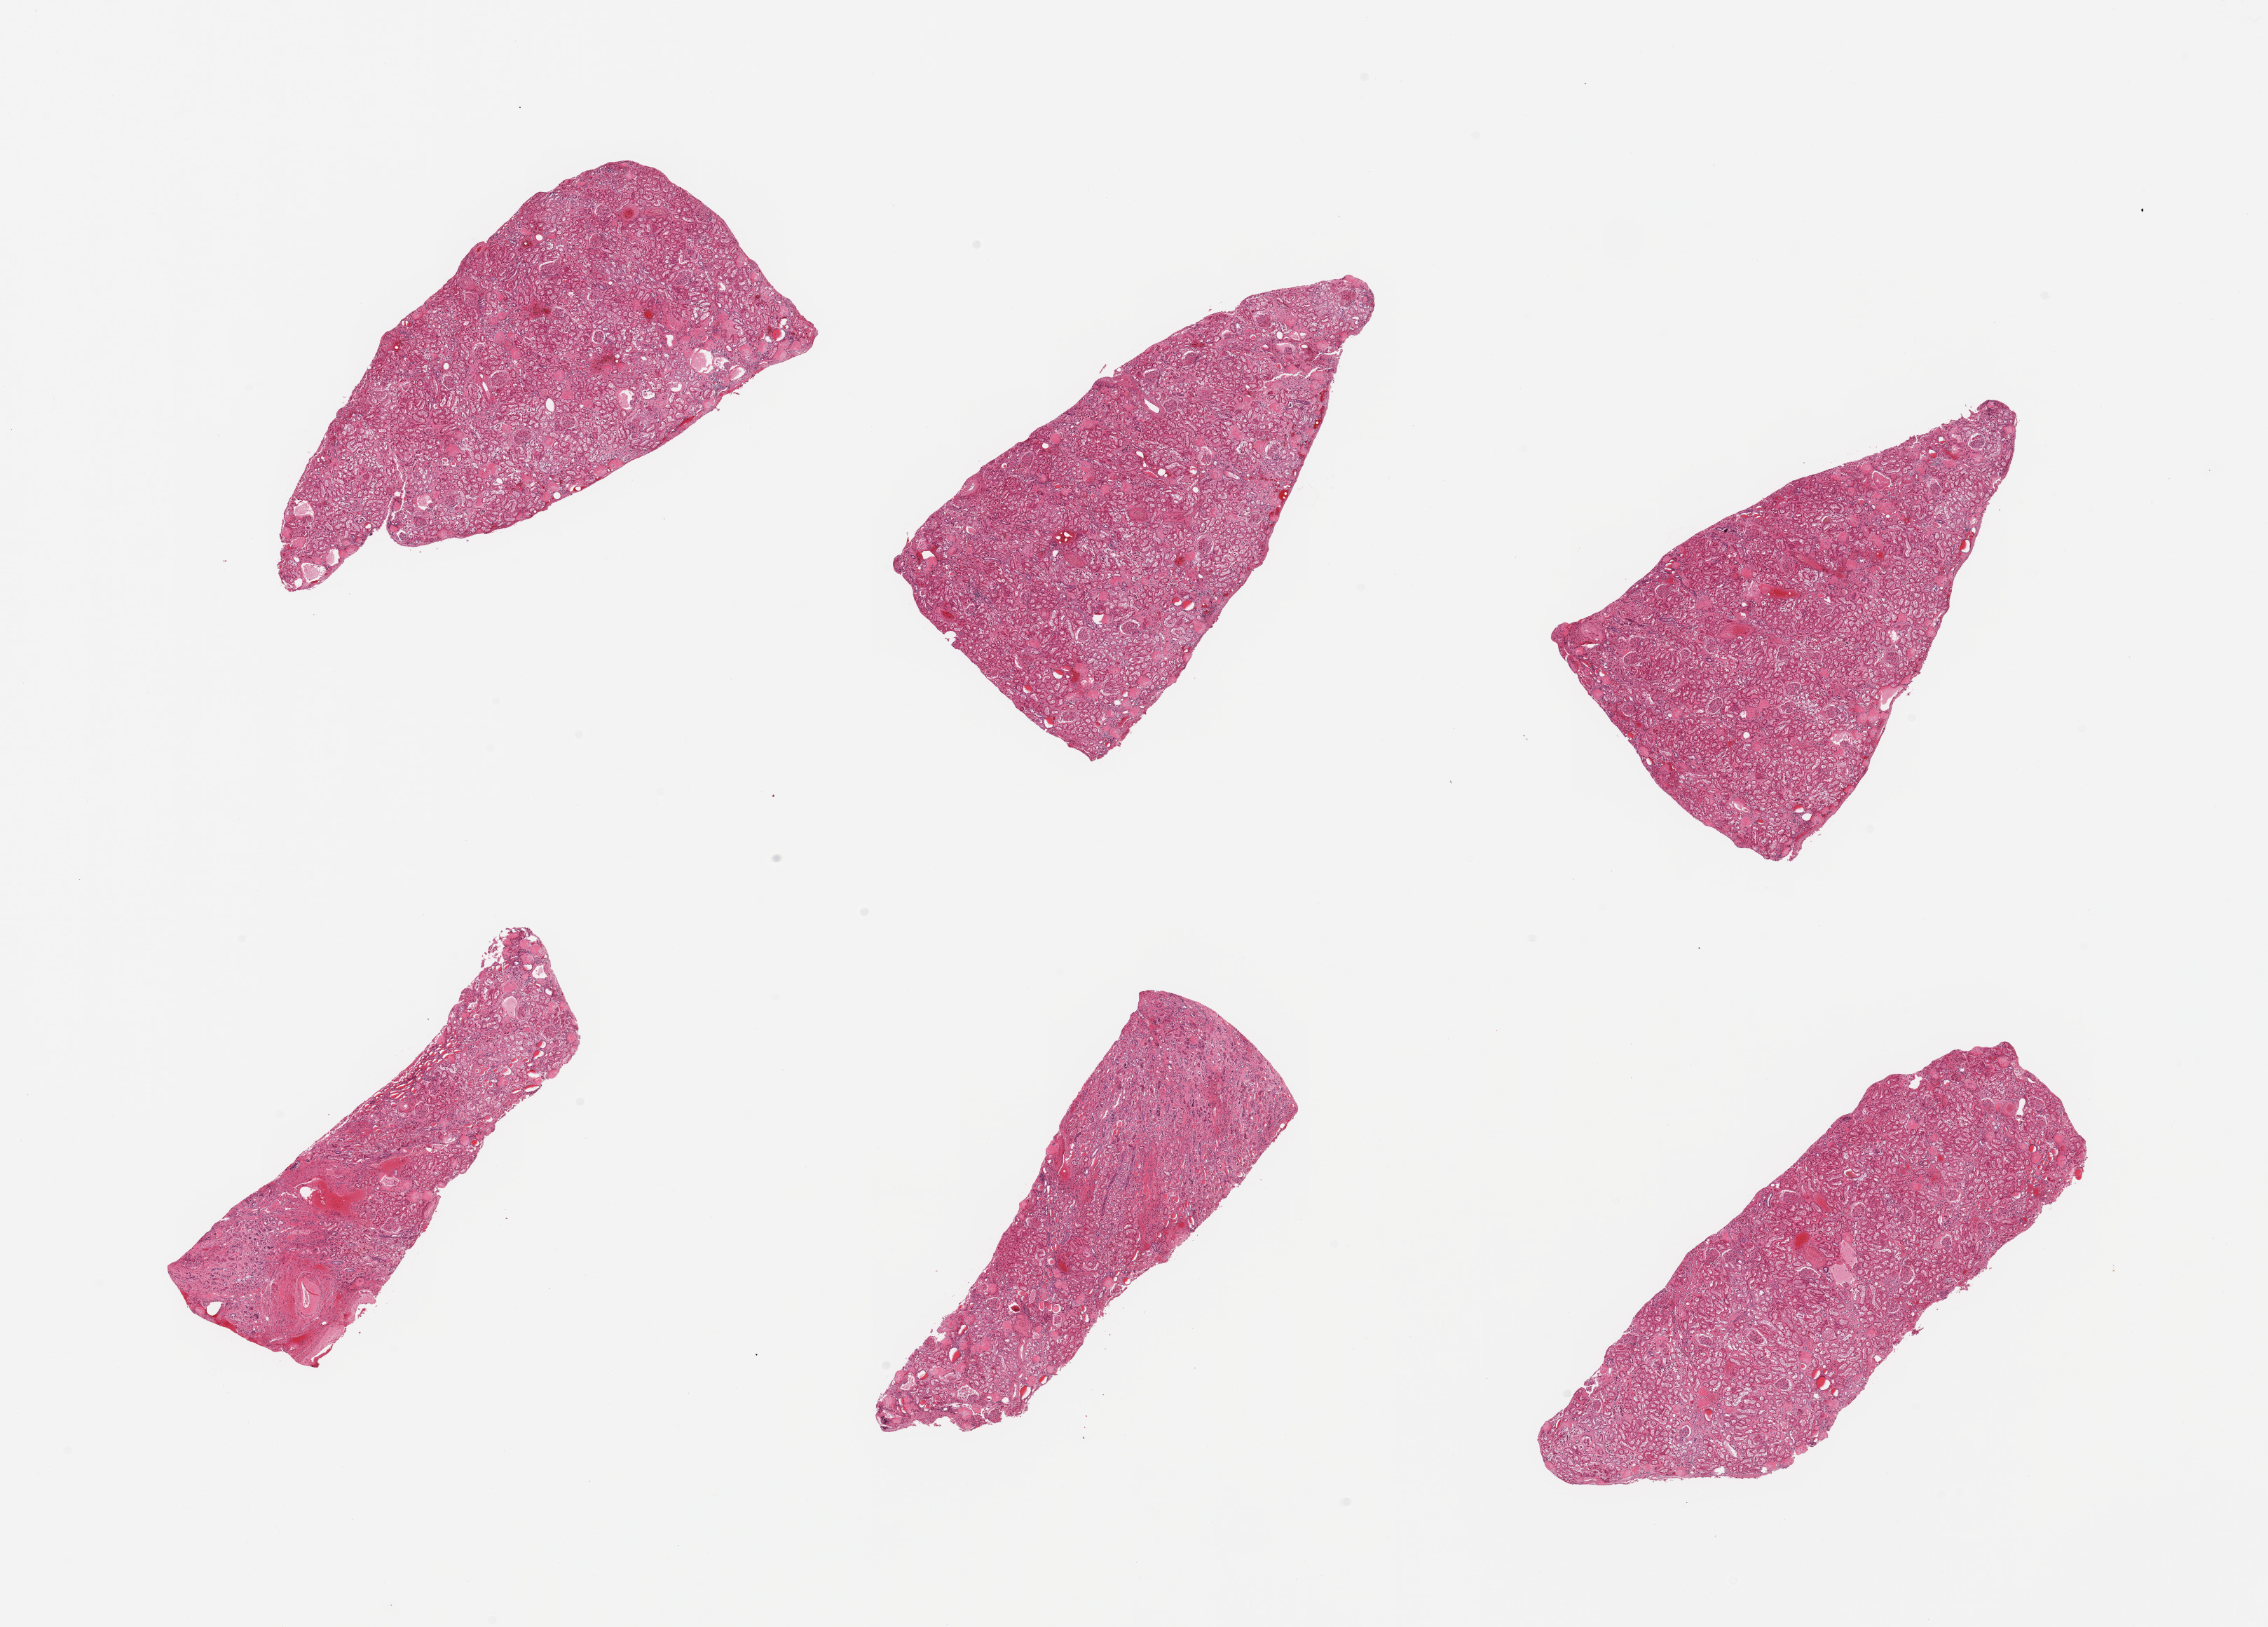
Hematoxylin and eosin (H&E) whole-slide image, a low-resolution overview of the entire scanned area, about 25.6 x 18.4 mm (from a 20x scan); PAXgene-fixed, paraffin-embedded tissue; section of renal cortex (target tissue); donor tissue sample. Male donor.
Reviewer comment on this tissue sample: 6 pieces; arterial sclerosis; 30% glomeruli sclerosed; hyalin casts.